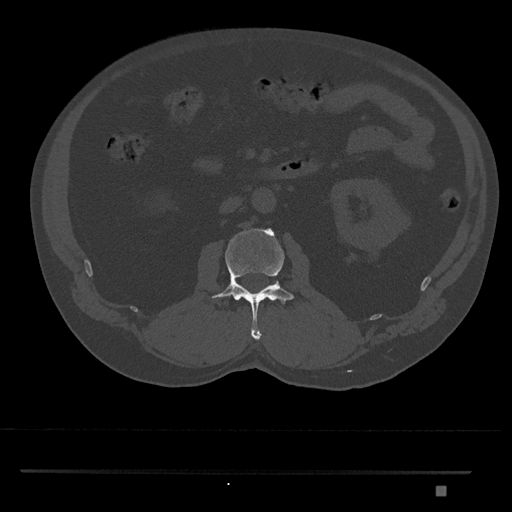
CT including the spine, one axial slice. Position 749 of 1134 along the scan axis. Reconstruction kernel Br40s/3. 120 kVp. Bone window (W 1800 / L 400 HU). 0.5 mm slice thickness. 512 × 512 image matrix, field of view 429 × 429 mm. Patient: male, 65 years. Case-level facts recorded for this patient, not image findings: primary cancer: prostate.
Outlined on this slice (semi-automatic segmentation, software-assisted and operator-edited):
- L2 vertebra: bounding box (x1, y1, x2, y2) in pixels: (211, 228, 295, 340)